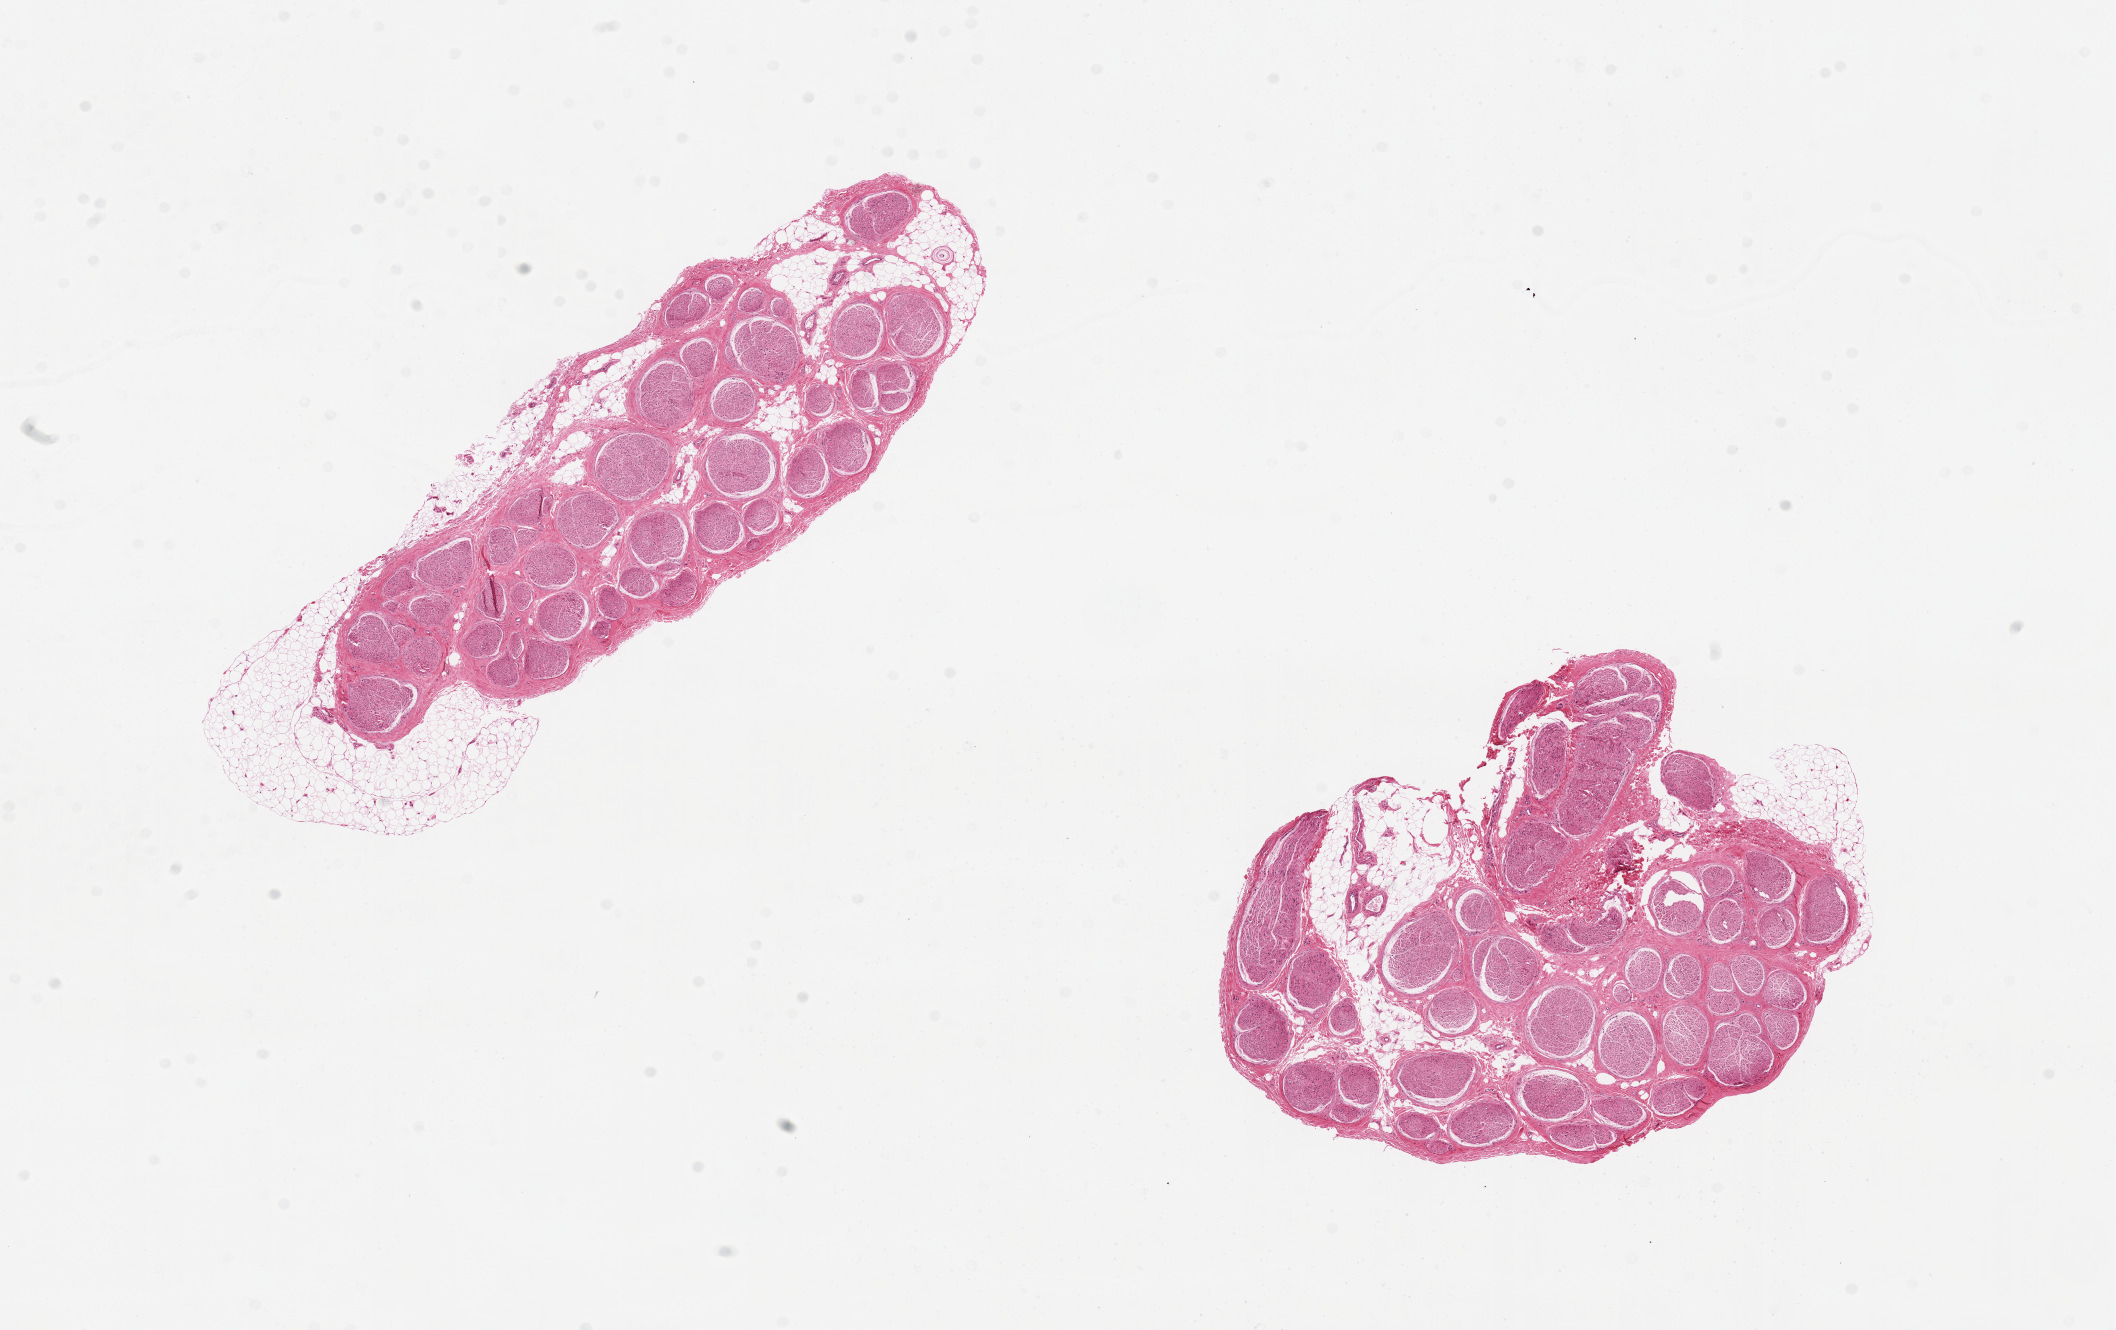
H&E whole-slide image, low-resolution overview of the scanned area, about 16.7 x 10.5 mm, PAXgene-fixed, paraffin-embedded tissue, section of tibial nerve (target tissue), tissue donor sample. Female donor.
* reviewer comment on this tissue sample: Nerve tissue is ~80% of specimen ; remainder fat ; (key says peripheral instead of tibial)